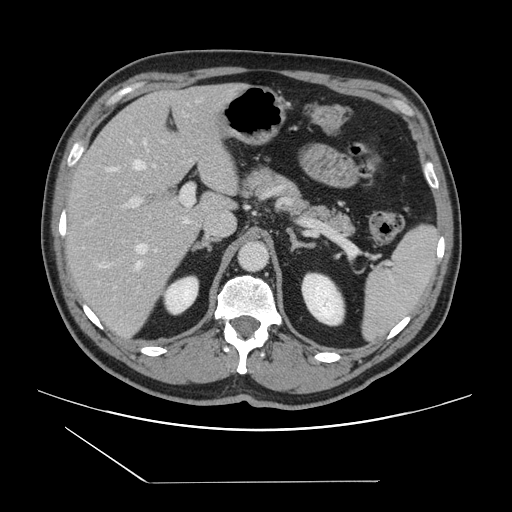
Contrast-enhanced abdominal CT, one axial slice. Position 90 of 157 along the scan axis. Intravenous contrast given. Soft-tissue window (W 400 / L 40 HU). 2.5 mm slice thickness. 512 × 512 image matrix, field of view 407 × 407 mm. Male patient, age 61 years. Case-level facts recorded for this patient, not image findings: diagnosis: colorectal cancer liver metastases, imaged before liver resection.
Structures marked on this image (expert manual segmentation):
- hepatic veins: bounding box [x1, y1, x2, y2] px = [100, 141, 148, 268]
- liver: [65, 85, 242, 338]
- planned liver remnant (the part of the liver to remain after resection): [66, 85, 235, 222]
- portal vein (with intrahepatic branches): [101, 184, 194, 265]